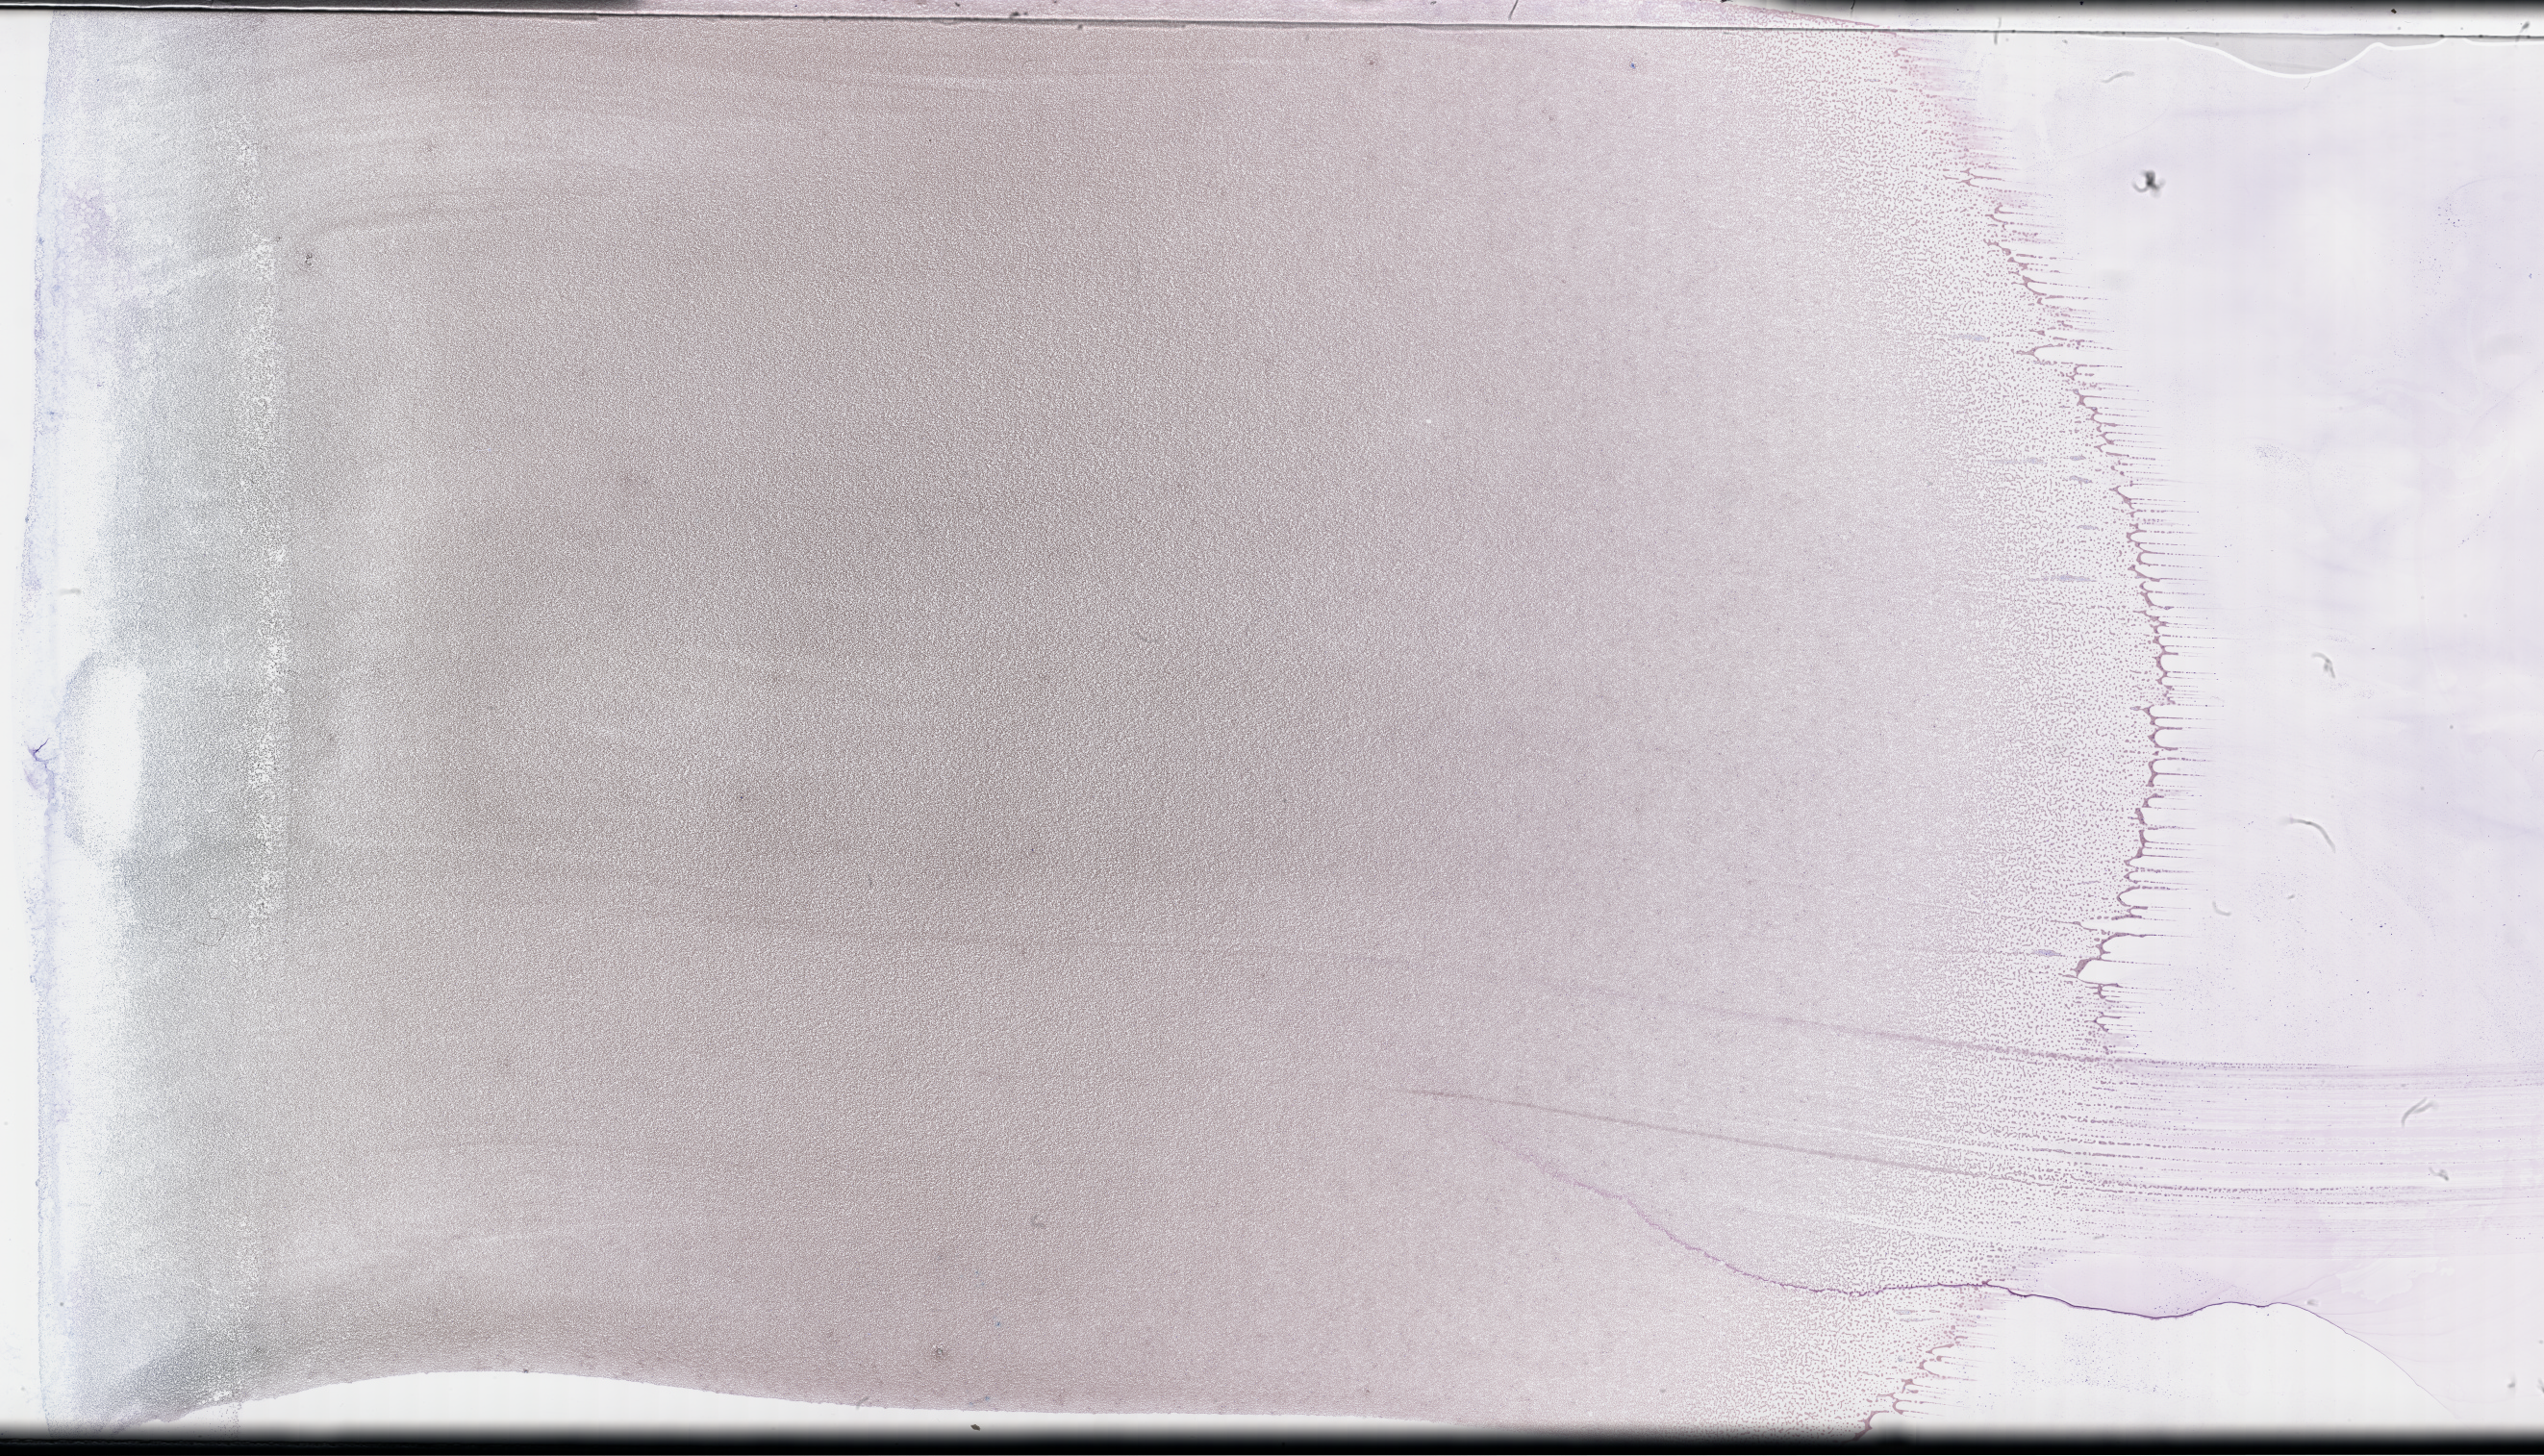
Whole-slide image of a whole blood smear, Wright–Giemsa stain, whole scanned area (about 42.7 x 24.5 mm) shown as a low-resolution overview; smear from an EDTA sample; specimen time point: collected on treatment. Patient: male.
From a patient with: Plasma Cell Myeloma.